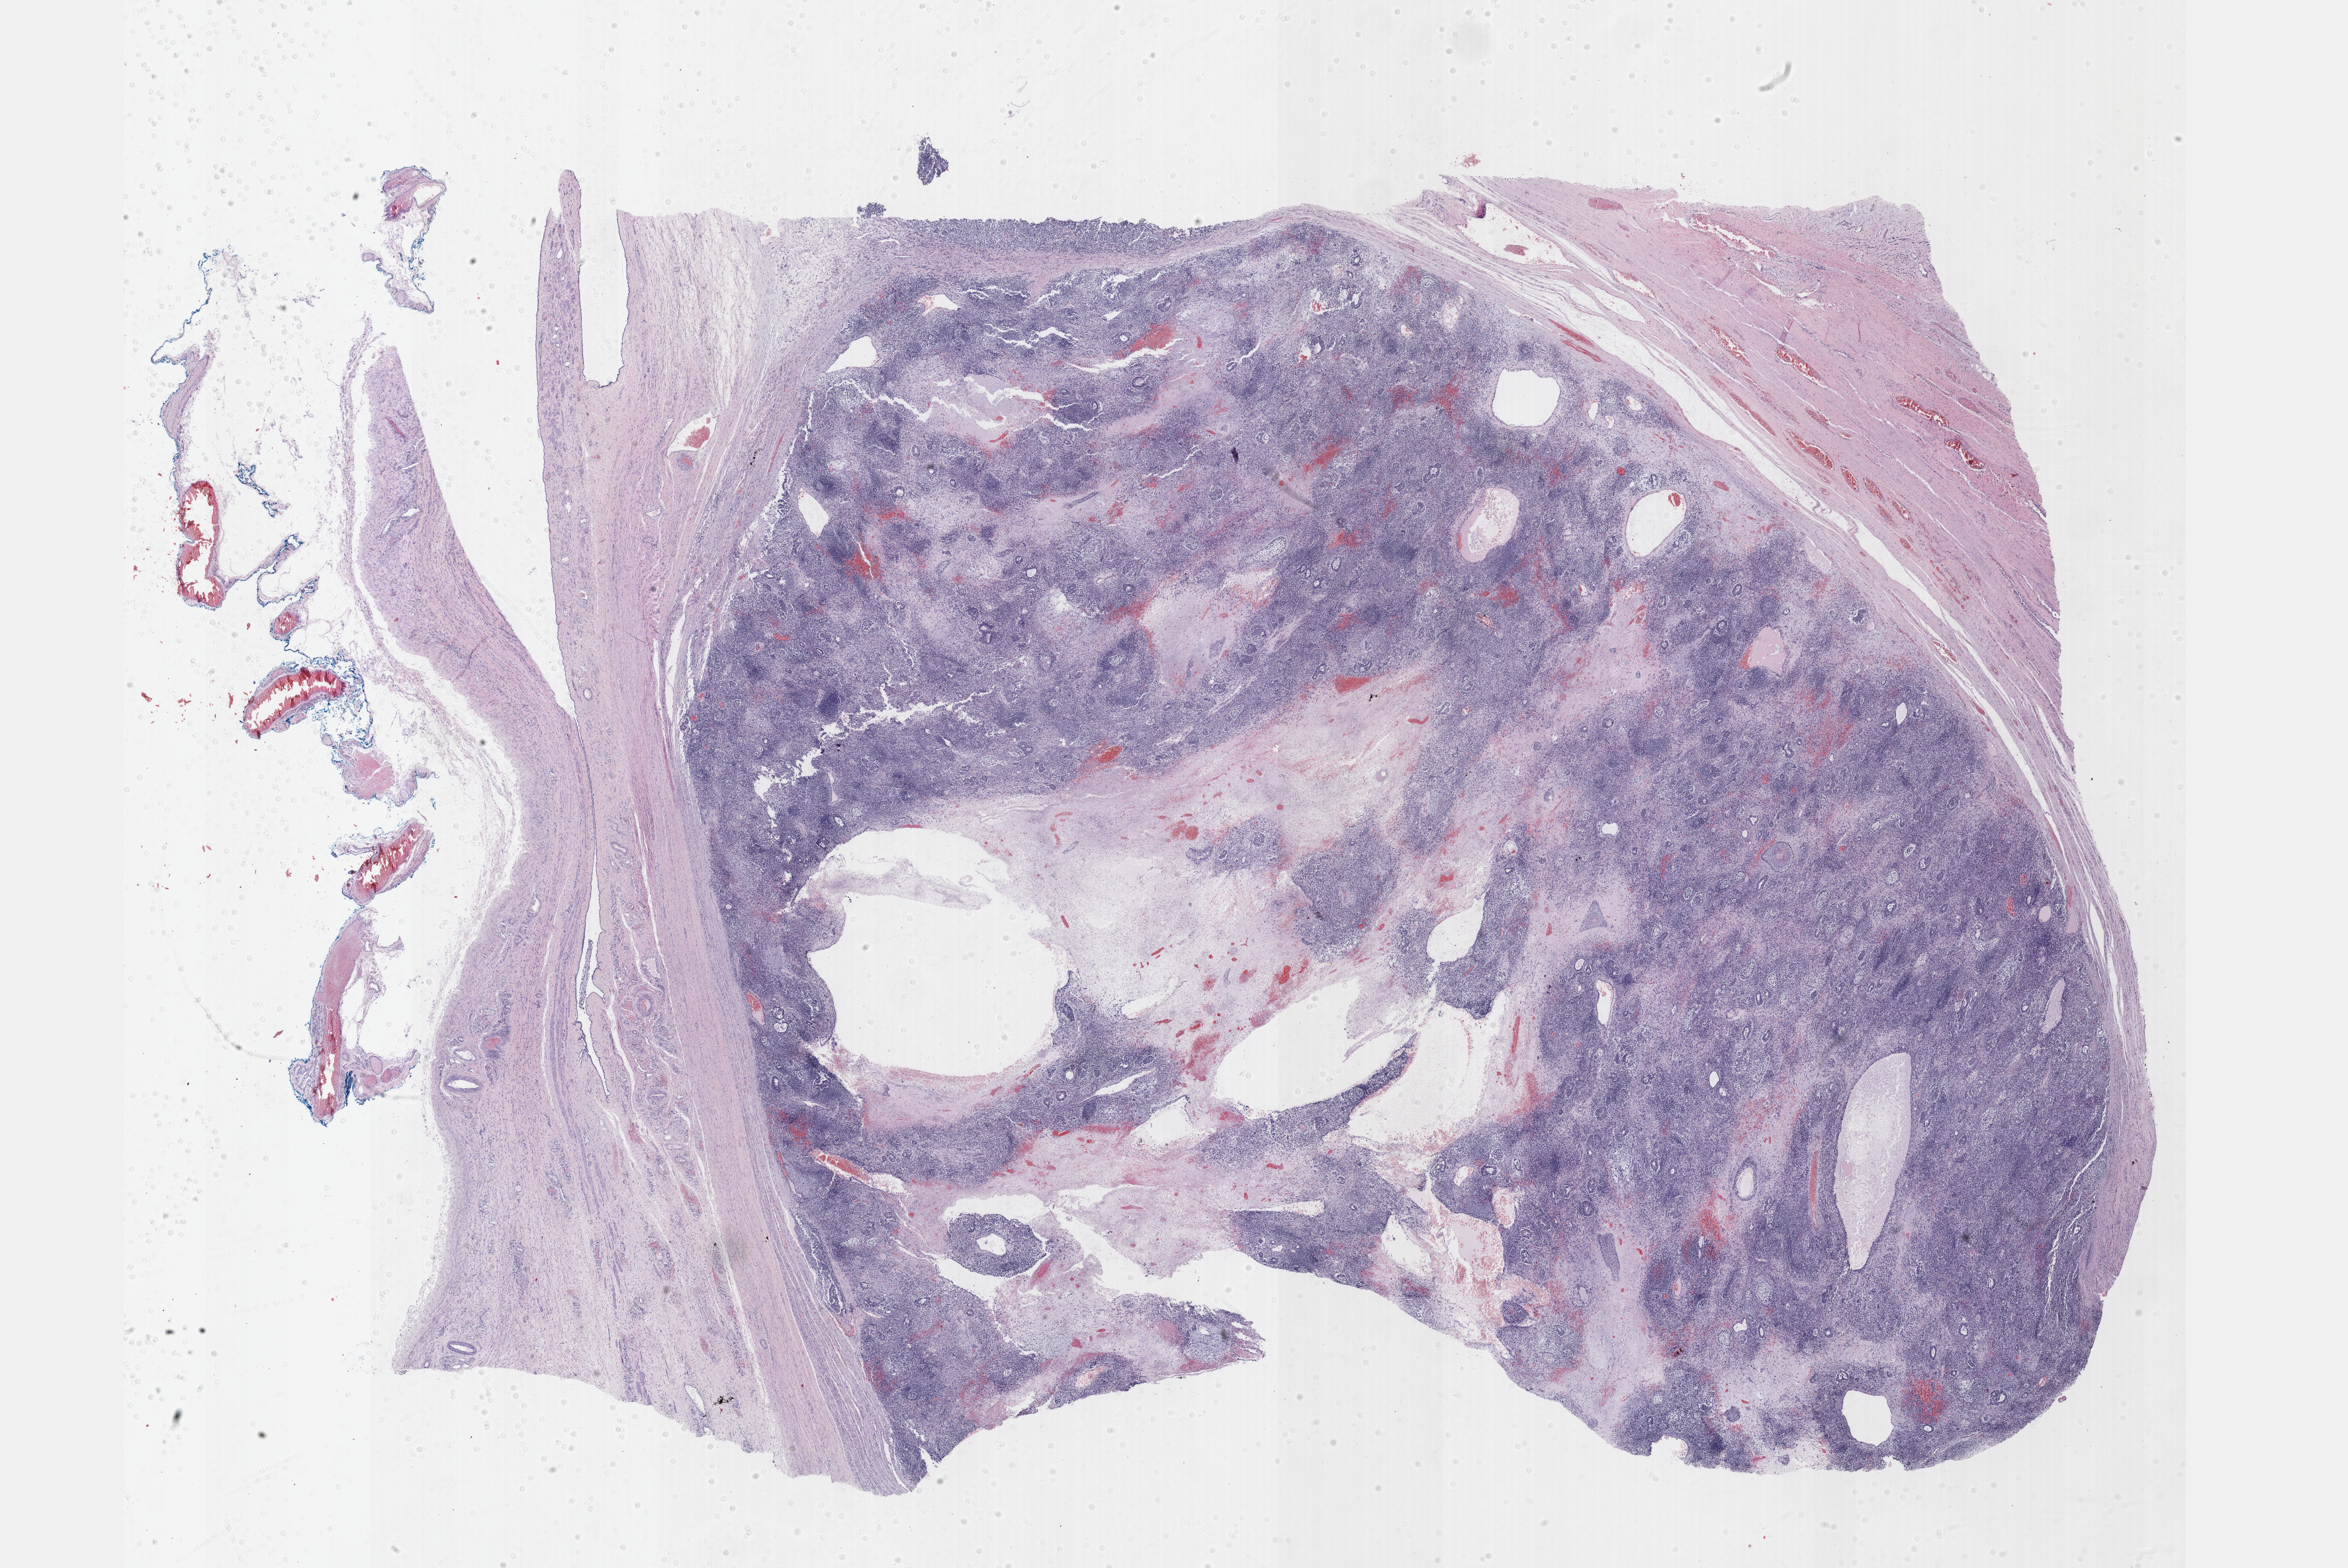
Whole-slide histology image, Hematoxylin and eosin (H&E) stained, shown as a low-resolution overview of the whole scanned area (about 28.7 x 19.2 mm); FFPE section; primary tumour sample from the testis. Male, age 21 years at initial diagnosis.
* diagnosis: Mixed germ cell tumor
* AJCC pathologic stage: IS (7th edition)
* laterality: right